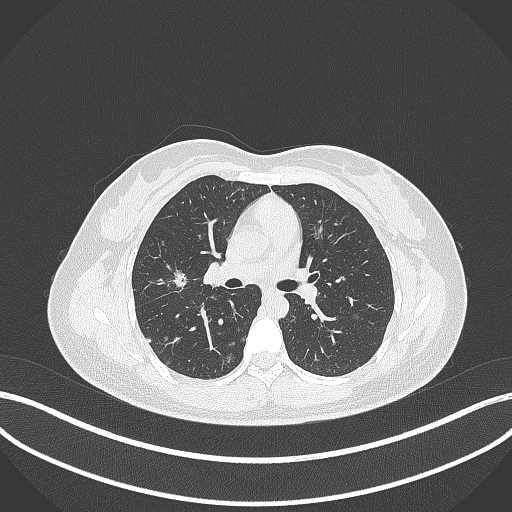
Chest CT, one axial slice. Slice 196 of 307 in the series (ordered by position). Reconstruction kernel B70f. Lung window (W 1500 / L -600 HU). 512 × 512 image matrix, field of view 400 × 400 mm. Patient: female, 33 years. Case-level facts recorded for this patient, not image findings: clinical TNM (as recorded): T1c N0 M0.
Structures marked on this image (rectangle marked by the reading radiologist):
- lung tumour (recorded histology: adenocarcinoma): bounding box [x1, y1, x2, y2] px = [169, 268, 189, 292]